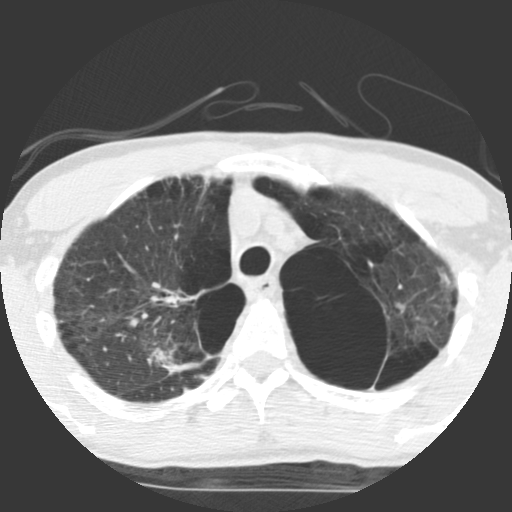
Chest CT (low-dose screening protocol), one axial image. First (baseline) screen. Lung window (W 1500 / L -600 HU). 2.5 mm slice thickness. Standard (soft-tissue) reconstruction kernel (STANDARD). 140 kVp. Male, age 62 years at enrolment.
Lesion marked by an expert reader, bounding box [x1, y1, x2, y2] px = [119, 324, 213, 392]. No non-calcified nodule or mass ≥4 mm was recorded by the screening reader at this exam.